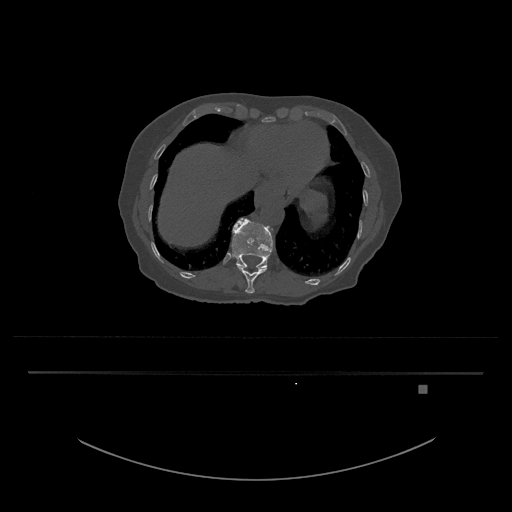
CT including the spine, one axial slice. Position 639 of 797 along the scan axis. Bone window (W 1800 / L 400 HU). 0.5 mm slice thickness. 512 × 512 image matrix, field of view 500 × 500 mm. Patient: female, 57 years. From the clinical record (not read from this slice): primary cancer: cervical.
Annotated regions visible in this slice (semi-automatically segmented with operator editing):
- T11 vertebra: box from (x=237, y=265) to (x=267, y=294) px
- T12 vertebra: (x=231, y=218)–(x=274, y=269)